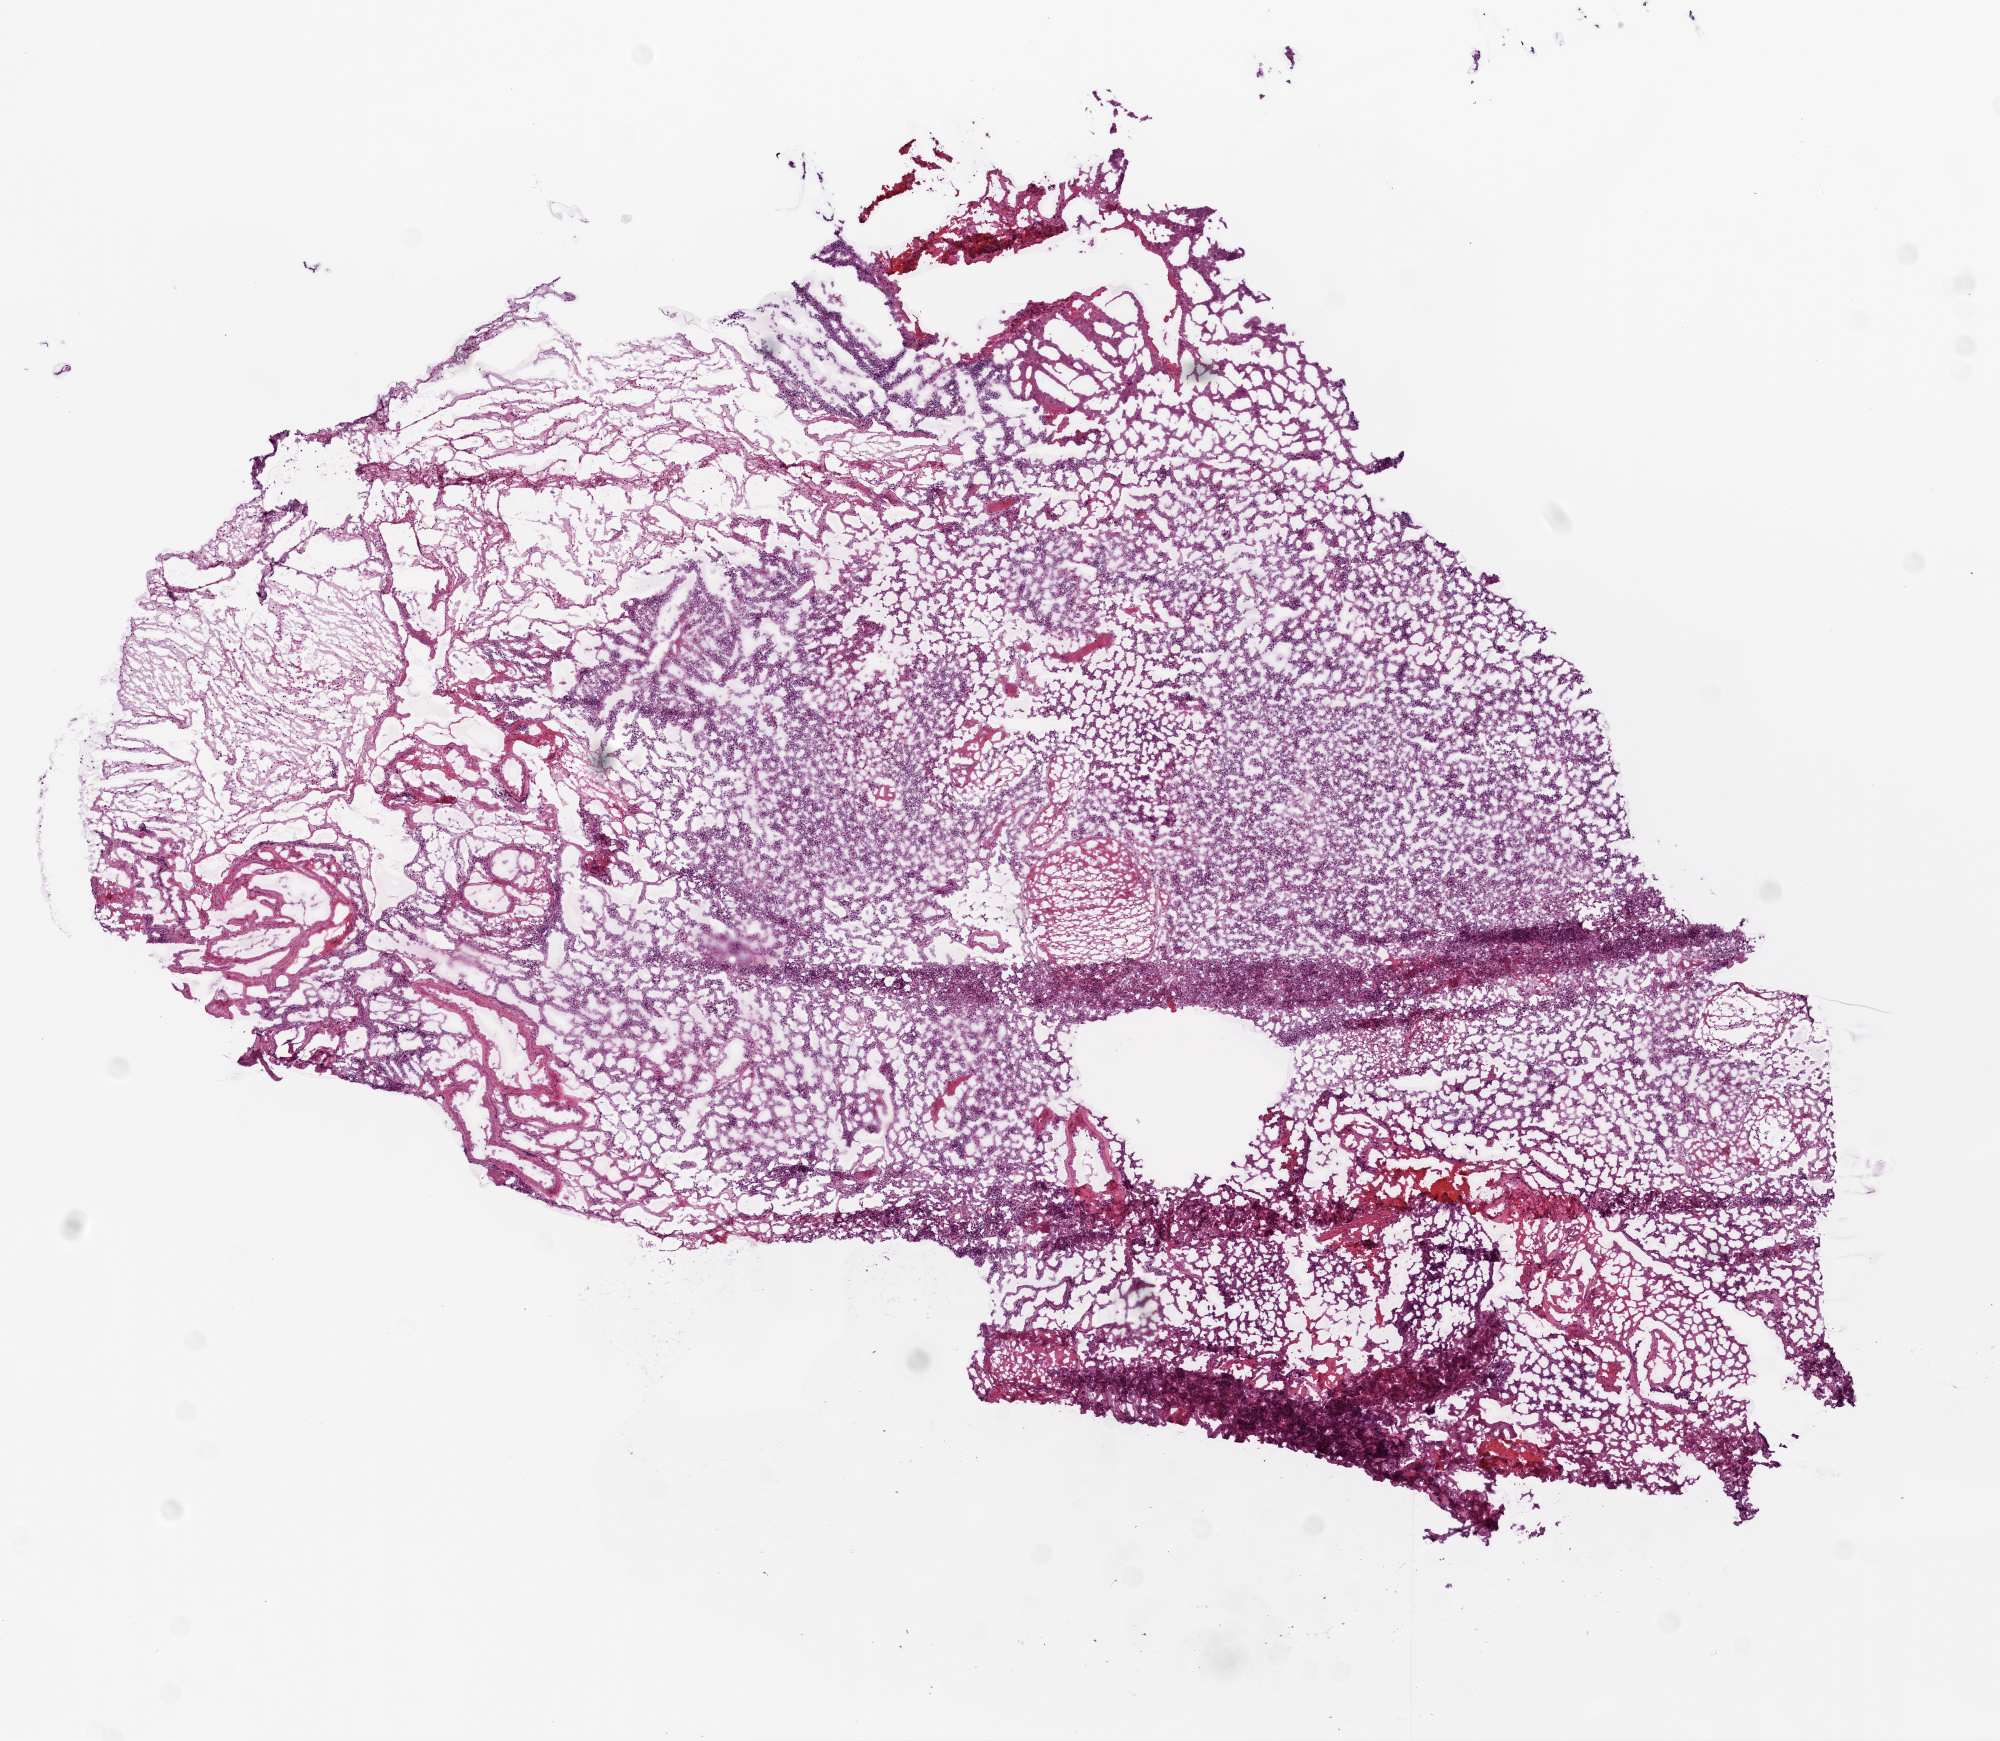
Digitized H&E-stained tissue section (whole slide), low-resolution overview of the scanned area, about 8.0 x 7.0 mm. Frozen section from the top of the tissue portion. Sample: primary tumour, brain. Female, age 52 years at initial diagnosis.
Diagnosis: Glioblastoma.